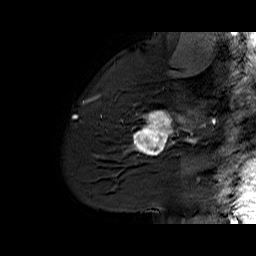
Breast MRI (dynamic contrast-enhanced), one sagittal slice. Position 46 of 60 along the scan axis. Dynamic contrast-enhanced series, time point 2 of 6 at this slice position (early post-contrast). 1.5 T. TE 6.1 ms, TR 32.9 ms. 256 × 256 image matrix. Female patient. Case-level facts recorded for this patient, not image findings: setting: breast cancer imaged before/during neoadjuvant chemotherapy; receptor status: HER2-positive.
Structures marked on this image (semi-automatically segmented with operator editing):
- analysis volume of interest (the breast-tissue region the enhancement analysis was run in; not a lesion): bounding box (x1, y1, x2, y2) in pixels: (127, 95, 194, 165)
- tumour enhancement mask (voxels above the 100 % enhancement threshold inside the analysis volume of interest): (127, 110, 192, 155)